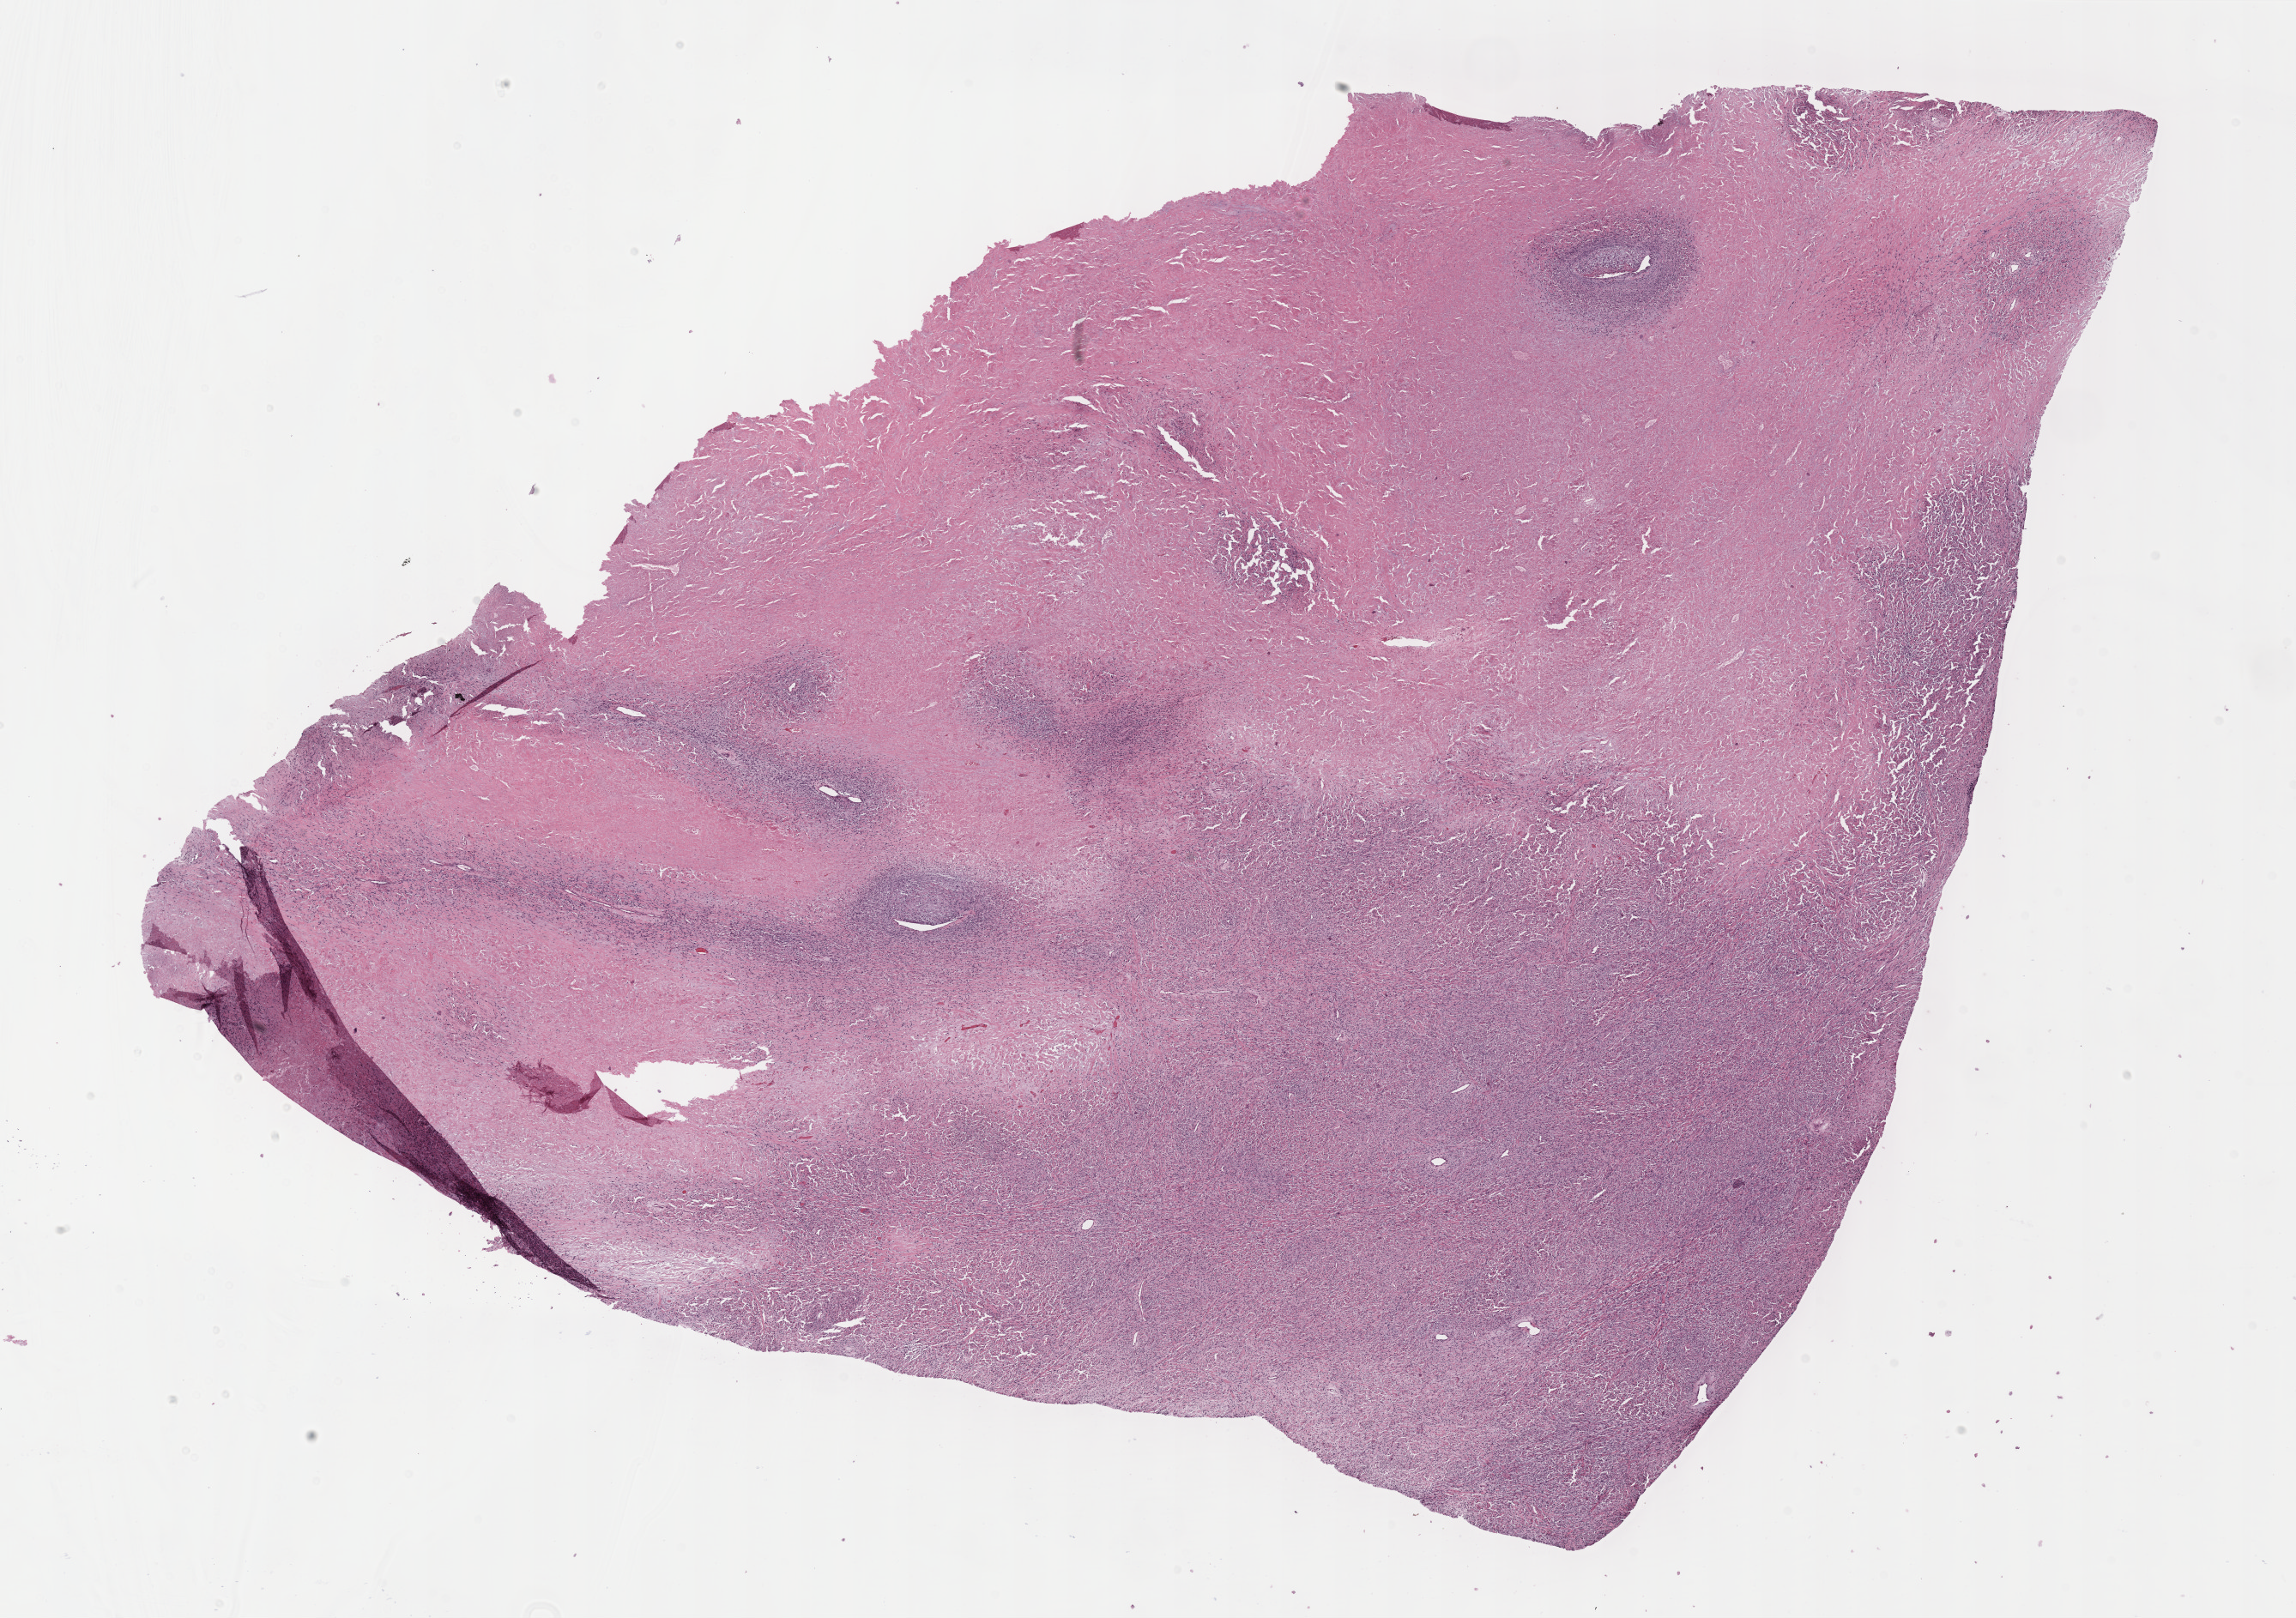
H&E whole-slide image, shown as a low-resolution overview of the whole scanned area (about 21.6 x 15.3 mm), FFPE section, sample: primary tumour, connective, subcutaneous and other soft tissues. Female, age 20 years at initial diagnosis.
Diagnosis: Malignant peripheral nerve sheath tumor (connective, subcutaneous and other soft tissues of lower limb and hip).